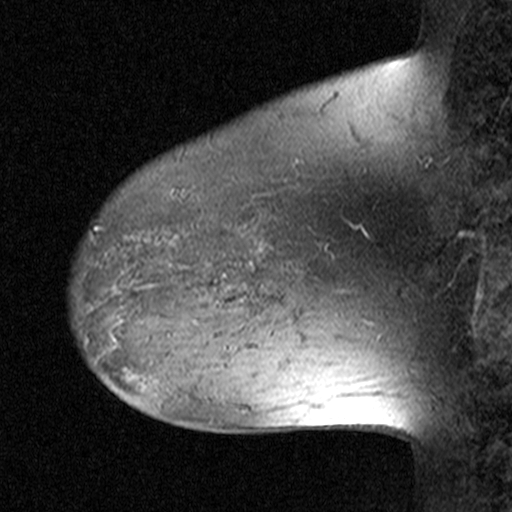
Breast MRI (dynamic contrast-enhanced), one sagittal slice. Slice 33 of 44 in the series (ordered by position). Dynamic contrast-enhanced study with each time point stored as its own series, time point 2 of 3 at this slice position (early post-contrast, ordered by acquisition time). 1.5 T. TE 4.5 ms, TR 11 ms. 3 mm slice thickness. 512 × 512 image matrix. Female patient, age 38 years. From the clinical record (not read from this slice): setting: breast cancer imaged before/during neoadjuvant chemotherapy; receptor status: HR-positive, HER2-negative.
Outlined on this slice (semi-automatically segmented with operator editing):
- analysis volume of interest (the breast-tissue region the enhancement analysis was run in; not a lesion): bounding box <152,236,253,335> (left, top, right, bottom; pixels)
- tumour enhancement mask (voxels above the 90 % enhancement threshold inside the analysis volume of interest): <215,299,219,304>